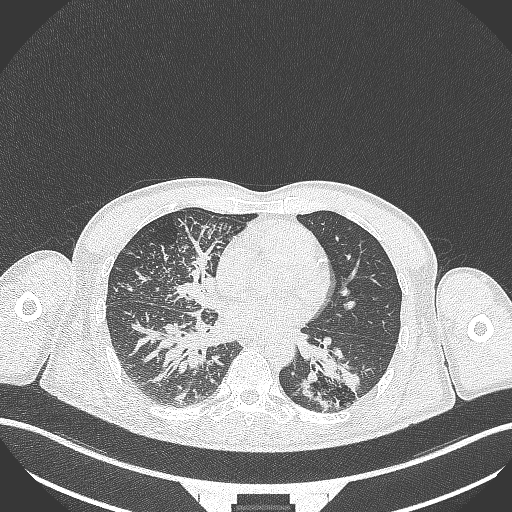
Chest CT, one axial slice. Slice 141 of 348 in the series (ordered by position). Reconstruction kernel B70f. 120 kVp. Lung window (W 1500 / L -600 HU). 1 mm slice thickness. 512 × 512 image matrix, field of view 400 × 400 mm. Patient: male, 49 years. From the clinical record (not read from this slice): clinical TNM (as recorded): T2b N1 M0.
Annotated regions visible in this slice (bounding box drawn by a radiologist):
- lung tumour (recorded histology: adenocarcinoma): box from (x=294, y=347) to (x=365, y=410) px